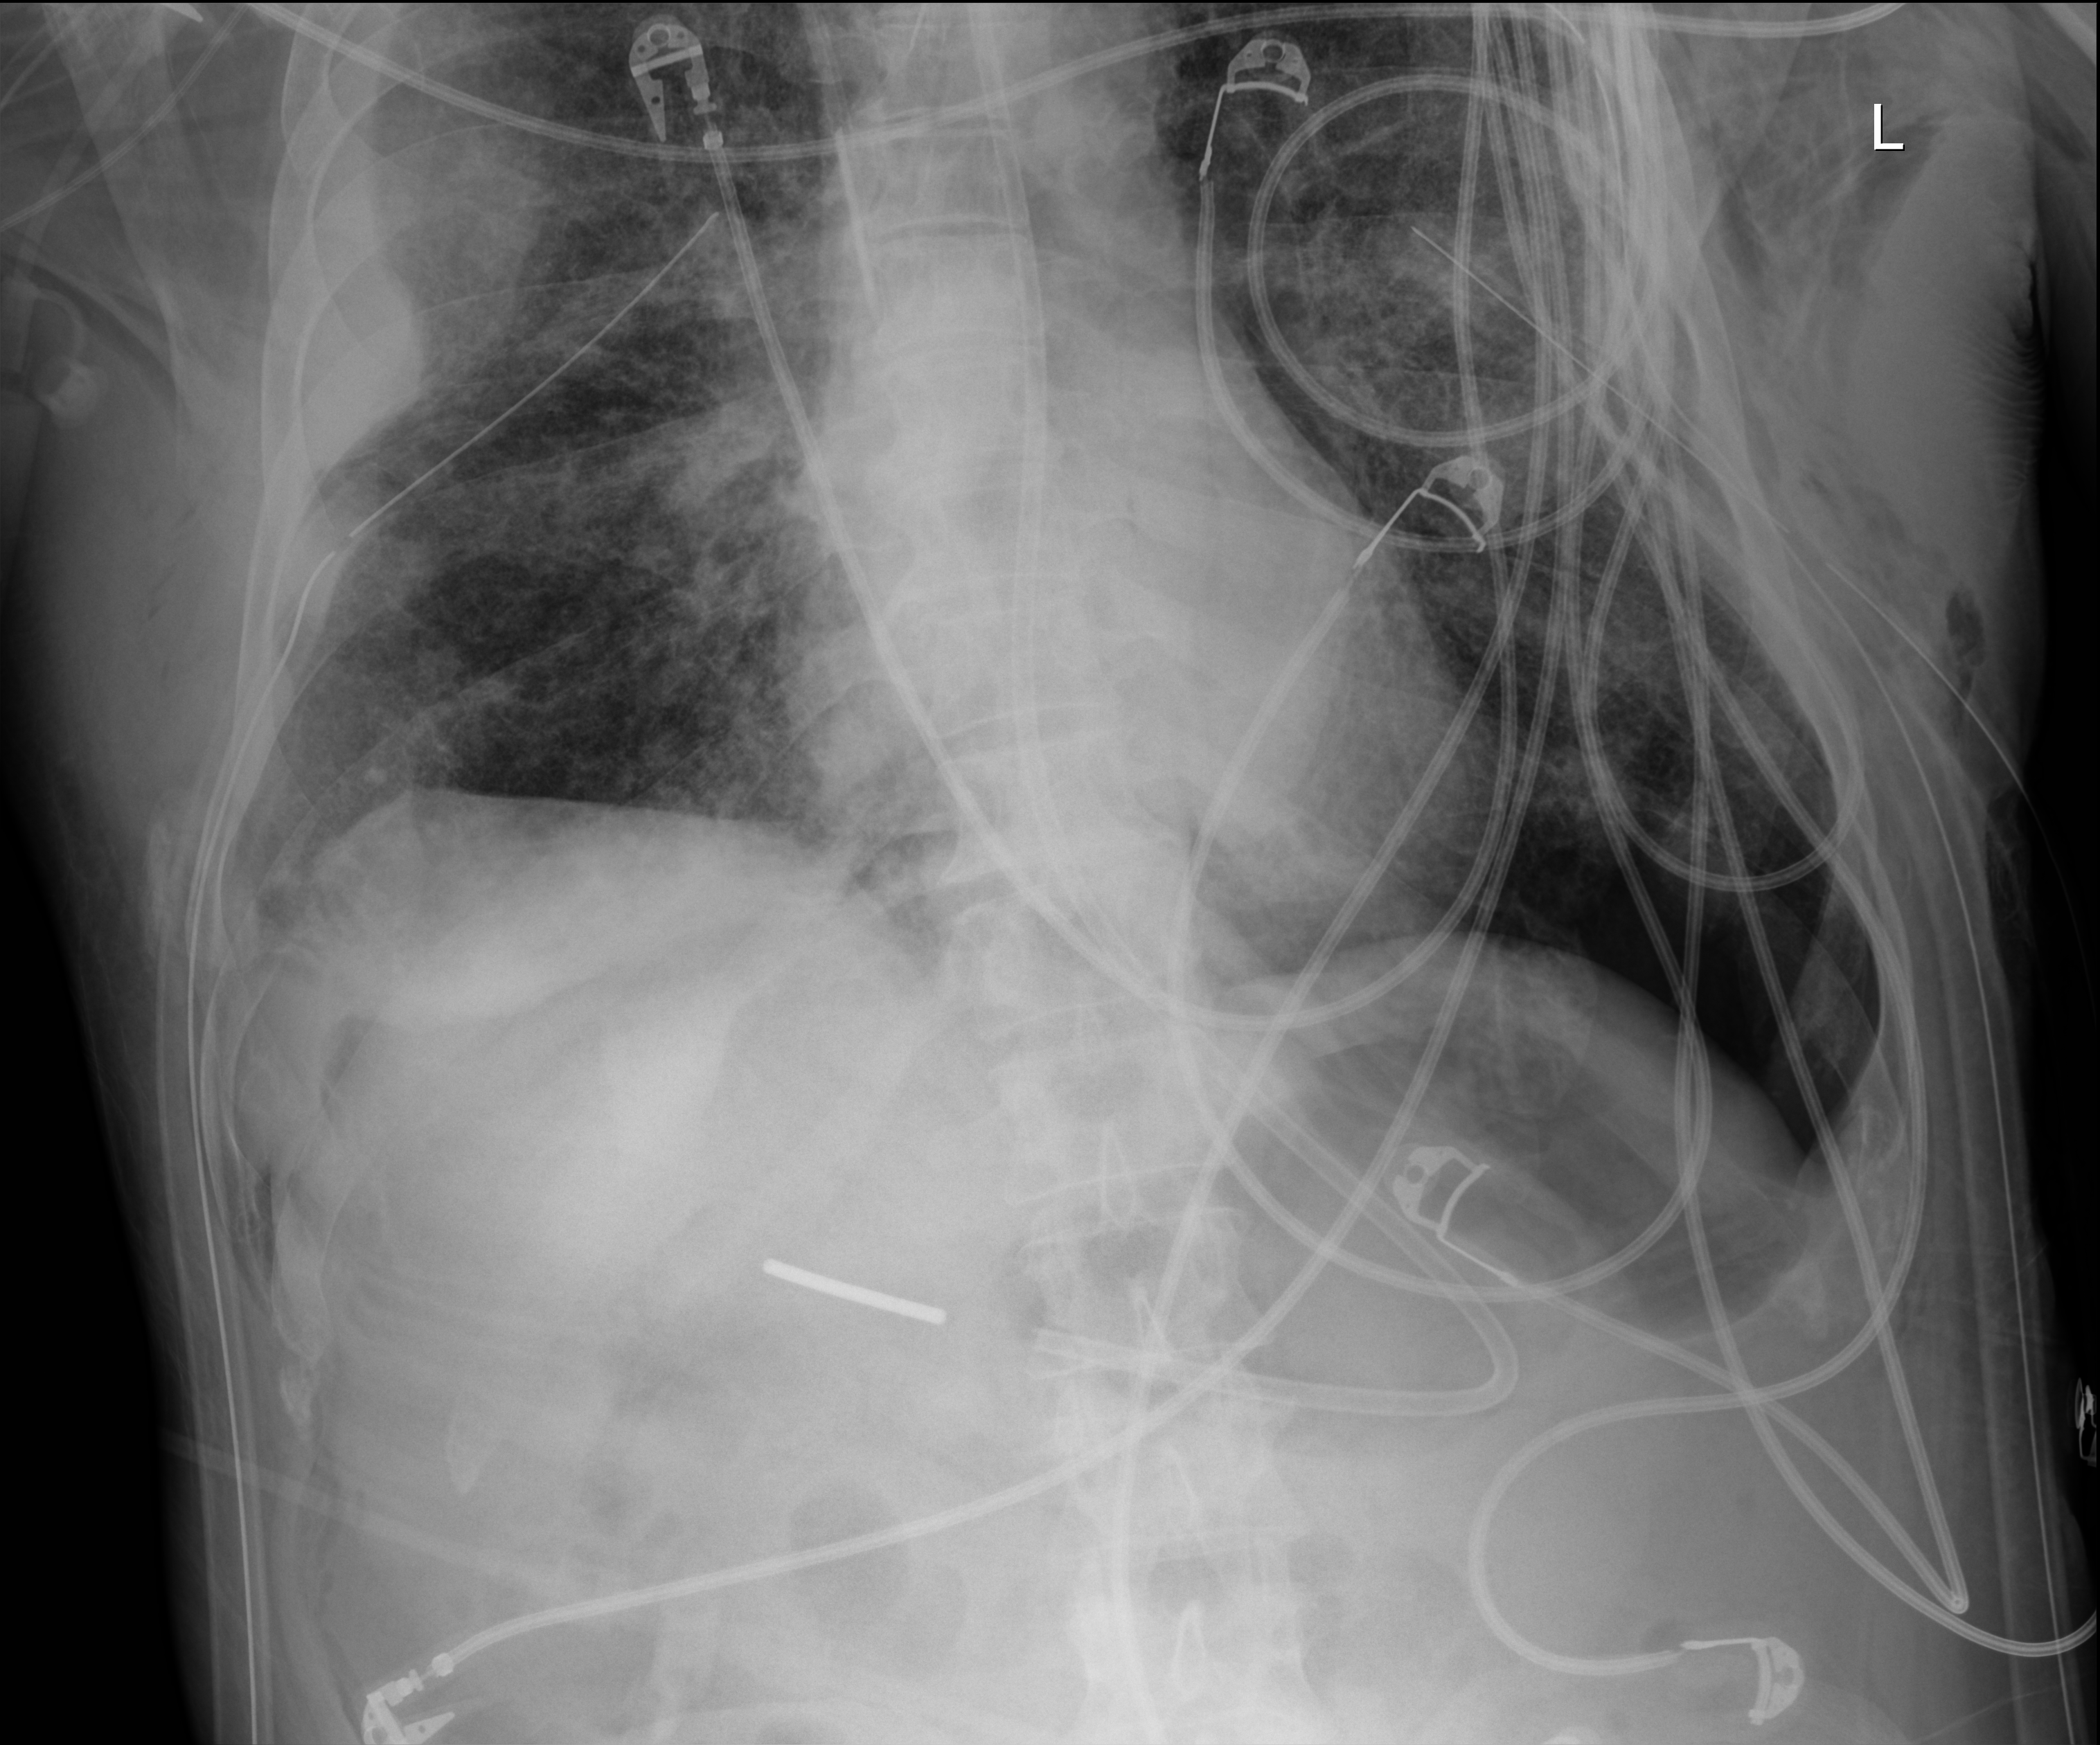
Bedside chest radiograph (digital radiography), anteroposterior (AP) projection. Patient hospitalised with COVID-19; male, aged 18–59 years.
From the hospital-stay record, not from the radiograph (when in the stay this image was taken is not recorded): chronic kidney disease (admission record): no; mechanically ventilated during this hospital stay: yes.